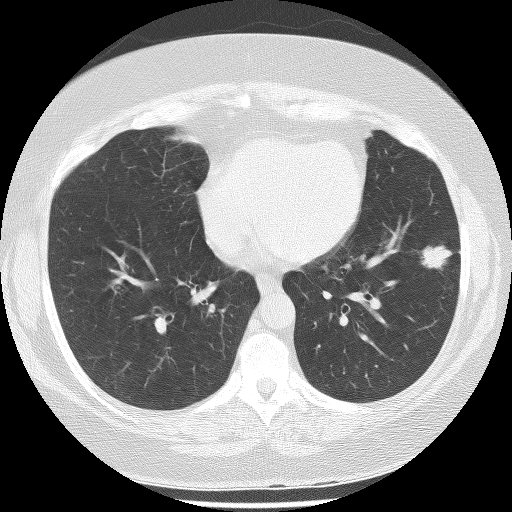
Axial slice from a low-dose chest CT screening exam. First (baseline) screen. Lung window (W 1500 / L -600 HU). Slice 131 of 233 in the series. 512 × 512 image matrix. Female, age 56 years at enrolment. Former smoker at enrolment.
- Expert reader's lesion annotation, bounding box <395,227,464,283> (left, top, right, bottom; pixels).
- The exam's reader record, not a measurement of the box and not confirmed to be the same lesion: non-calcified nodule or mass ≥4 mm, left lower lobe, 22 × 17 mm, spiculated (stellate) margins, soft tissue attenuation.
- Participant outcome: lung cancer diagnosed 63 days after this screen — bronchiolo-alveolar adenocarcinoma, NOS, left lower lobe, stage IA (AJCC 6th edition), 18 mm at pathology.